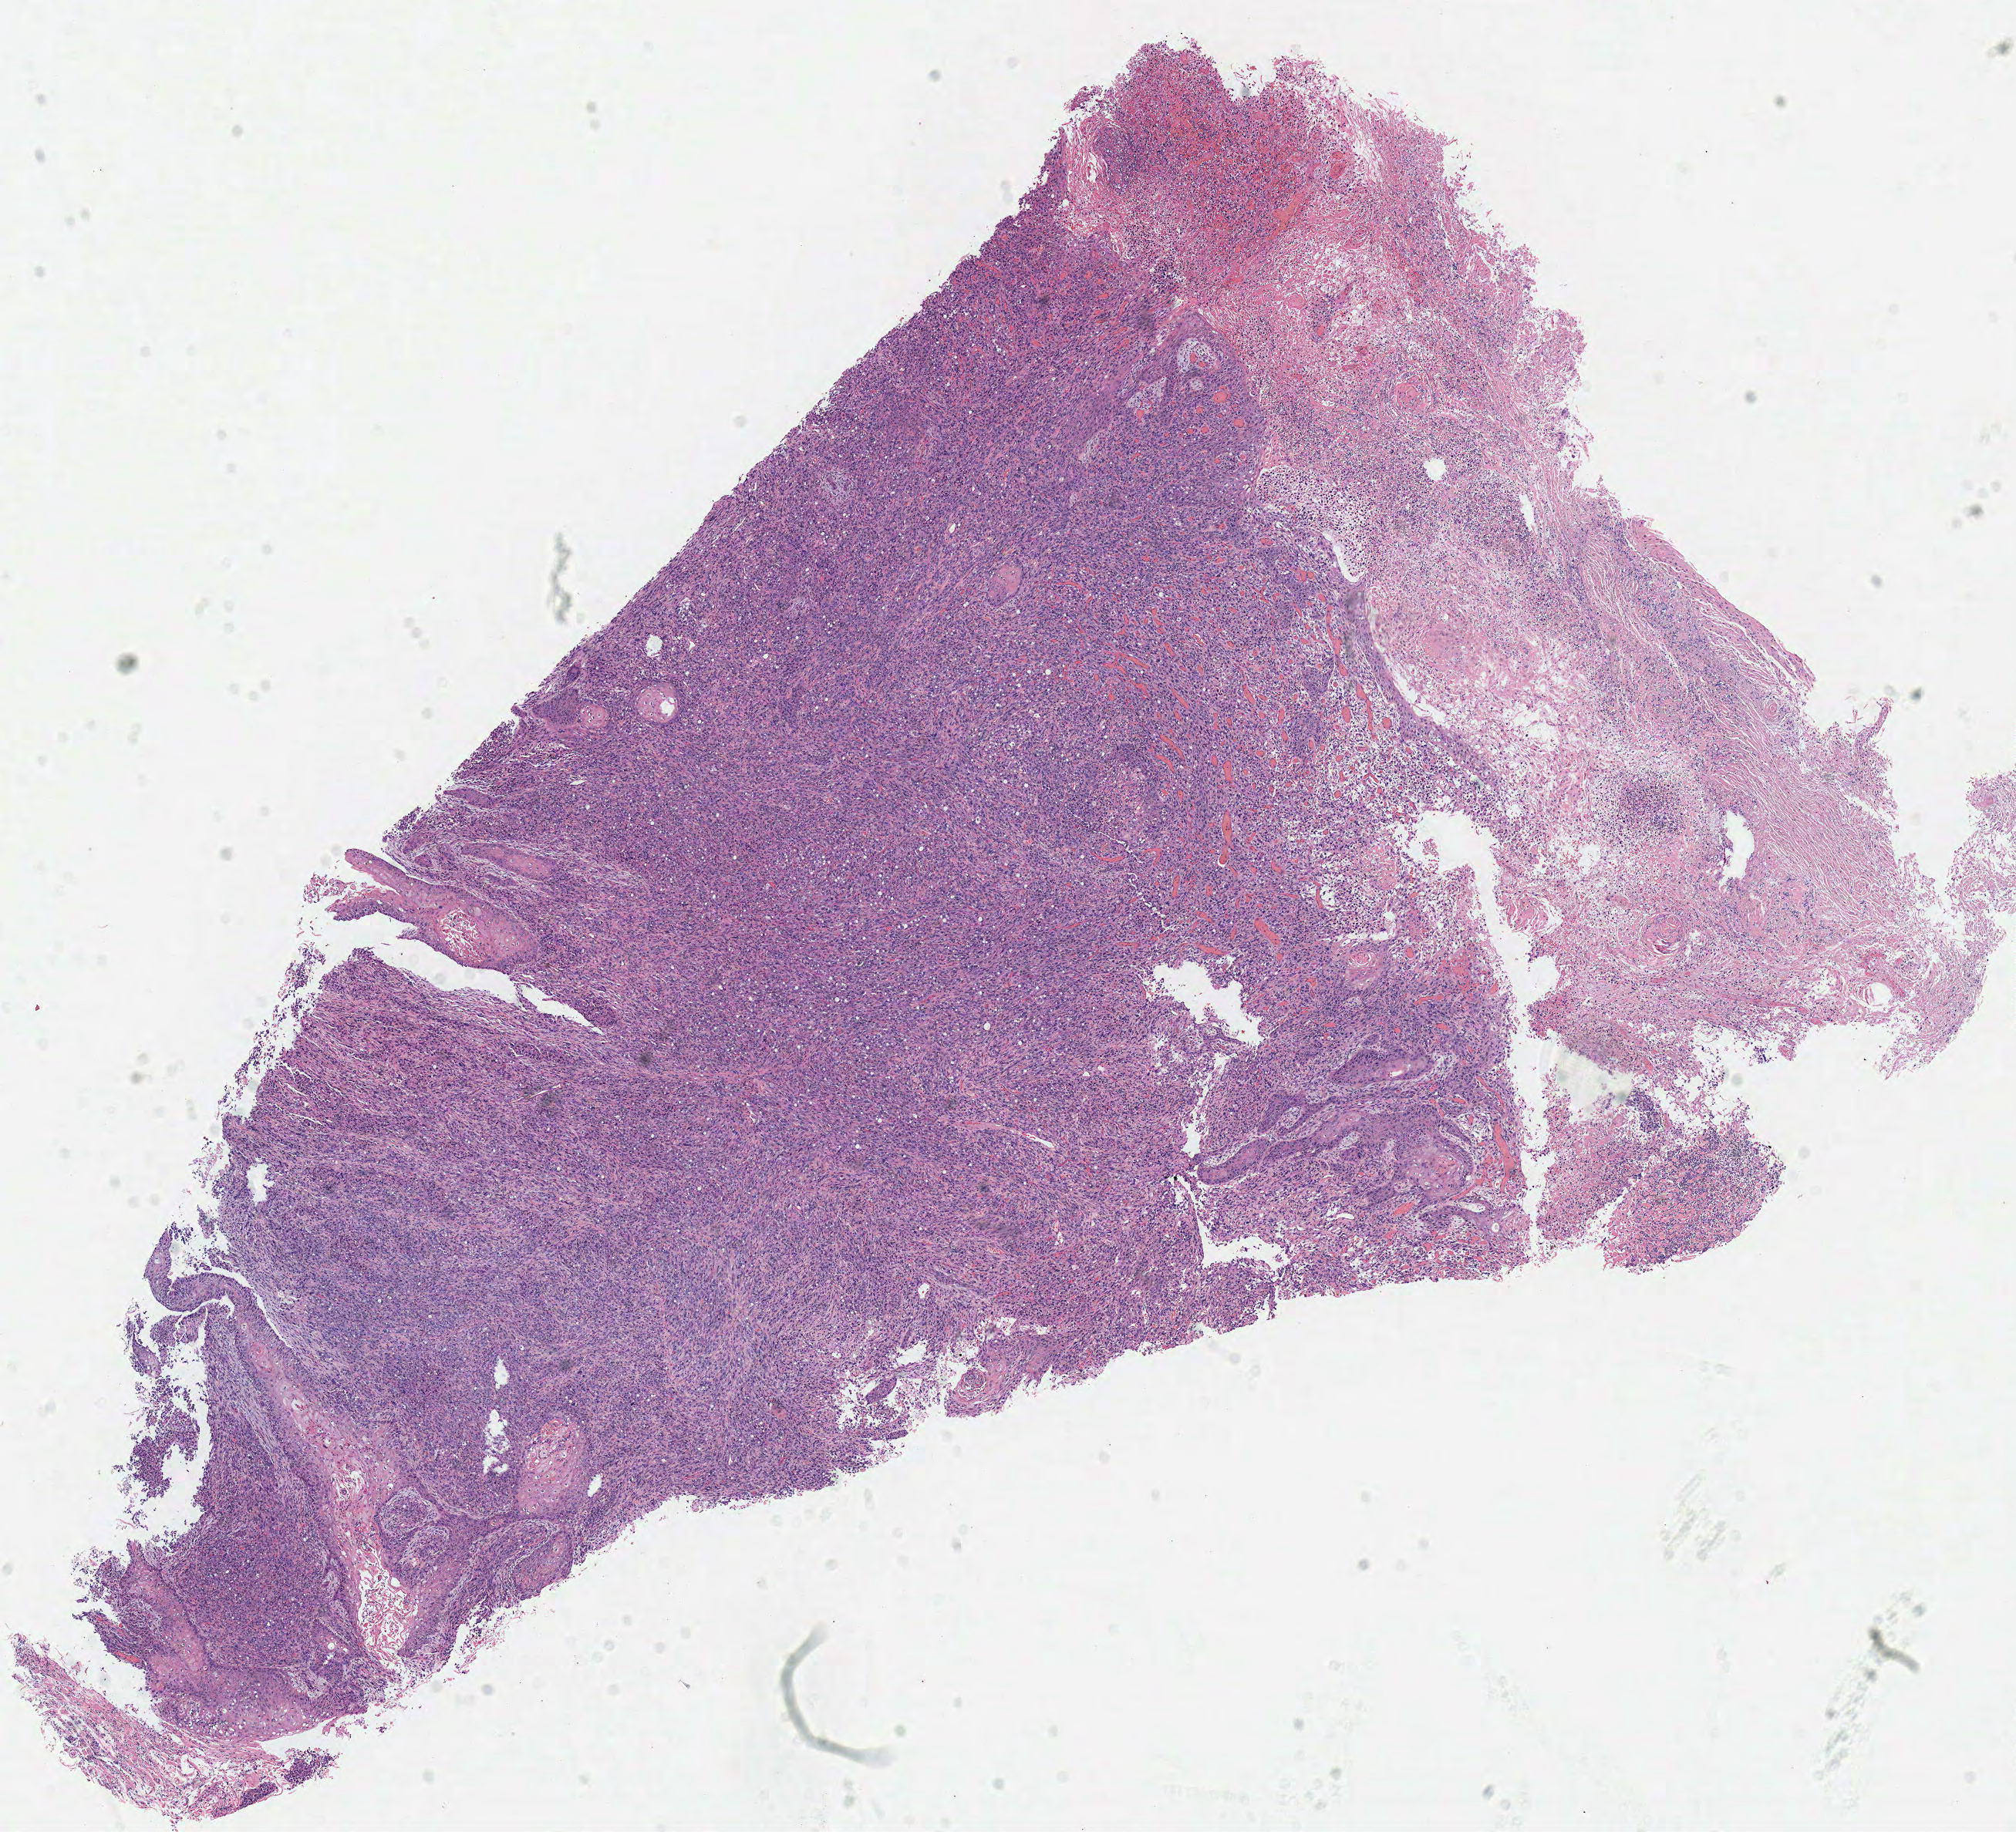
Digitized Hematoxylin and eosin (H&E) stained tissue section (whole slide) — shown as a low-resolution overview of the whole scanned area (about 10.3 x 9.3 mm, slide scanned at 40x); frozen section from the top of the tissue portion; primary tumour sample from the lung. Patient: male, age at initial diagnosis 85 years. Slide review estimates, as recorded: tumour cells 100%, tumour nuclei 80%, normal cells 0%, stromal cells 0%, necrosis 0%. Inflammatory infiltration, as recorded: lymphocyte infiltration 5%, monocyte infiltration 0%, neutrophil infiltration 10%.
AJCC pathologic stage: IB (6th edition). Pathologic diagnosis: Squamous cell carcinoma, NOS (upper lobe, lung).